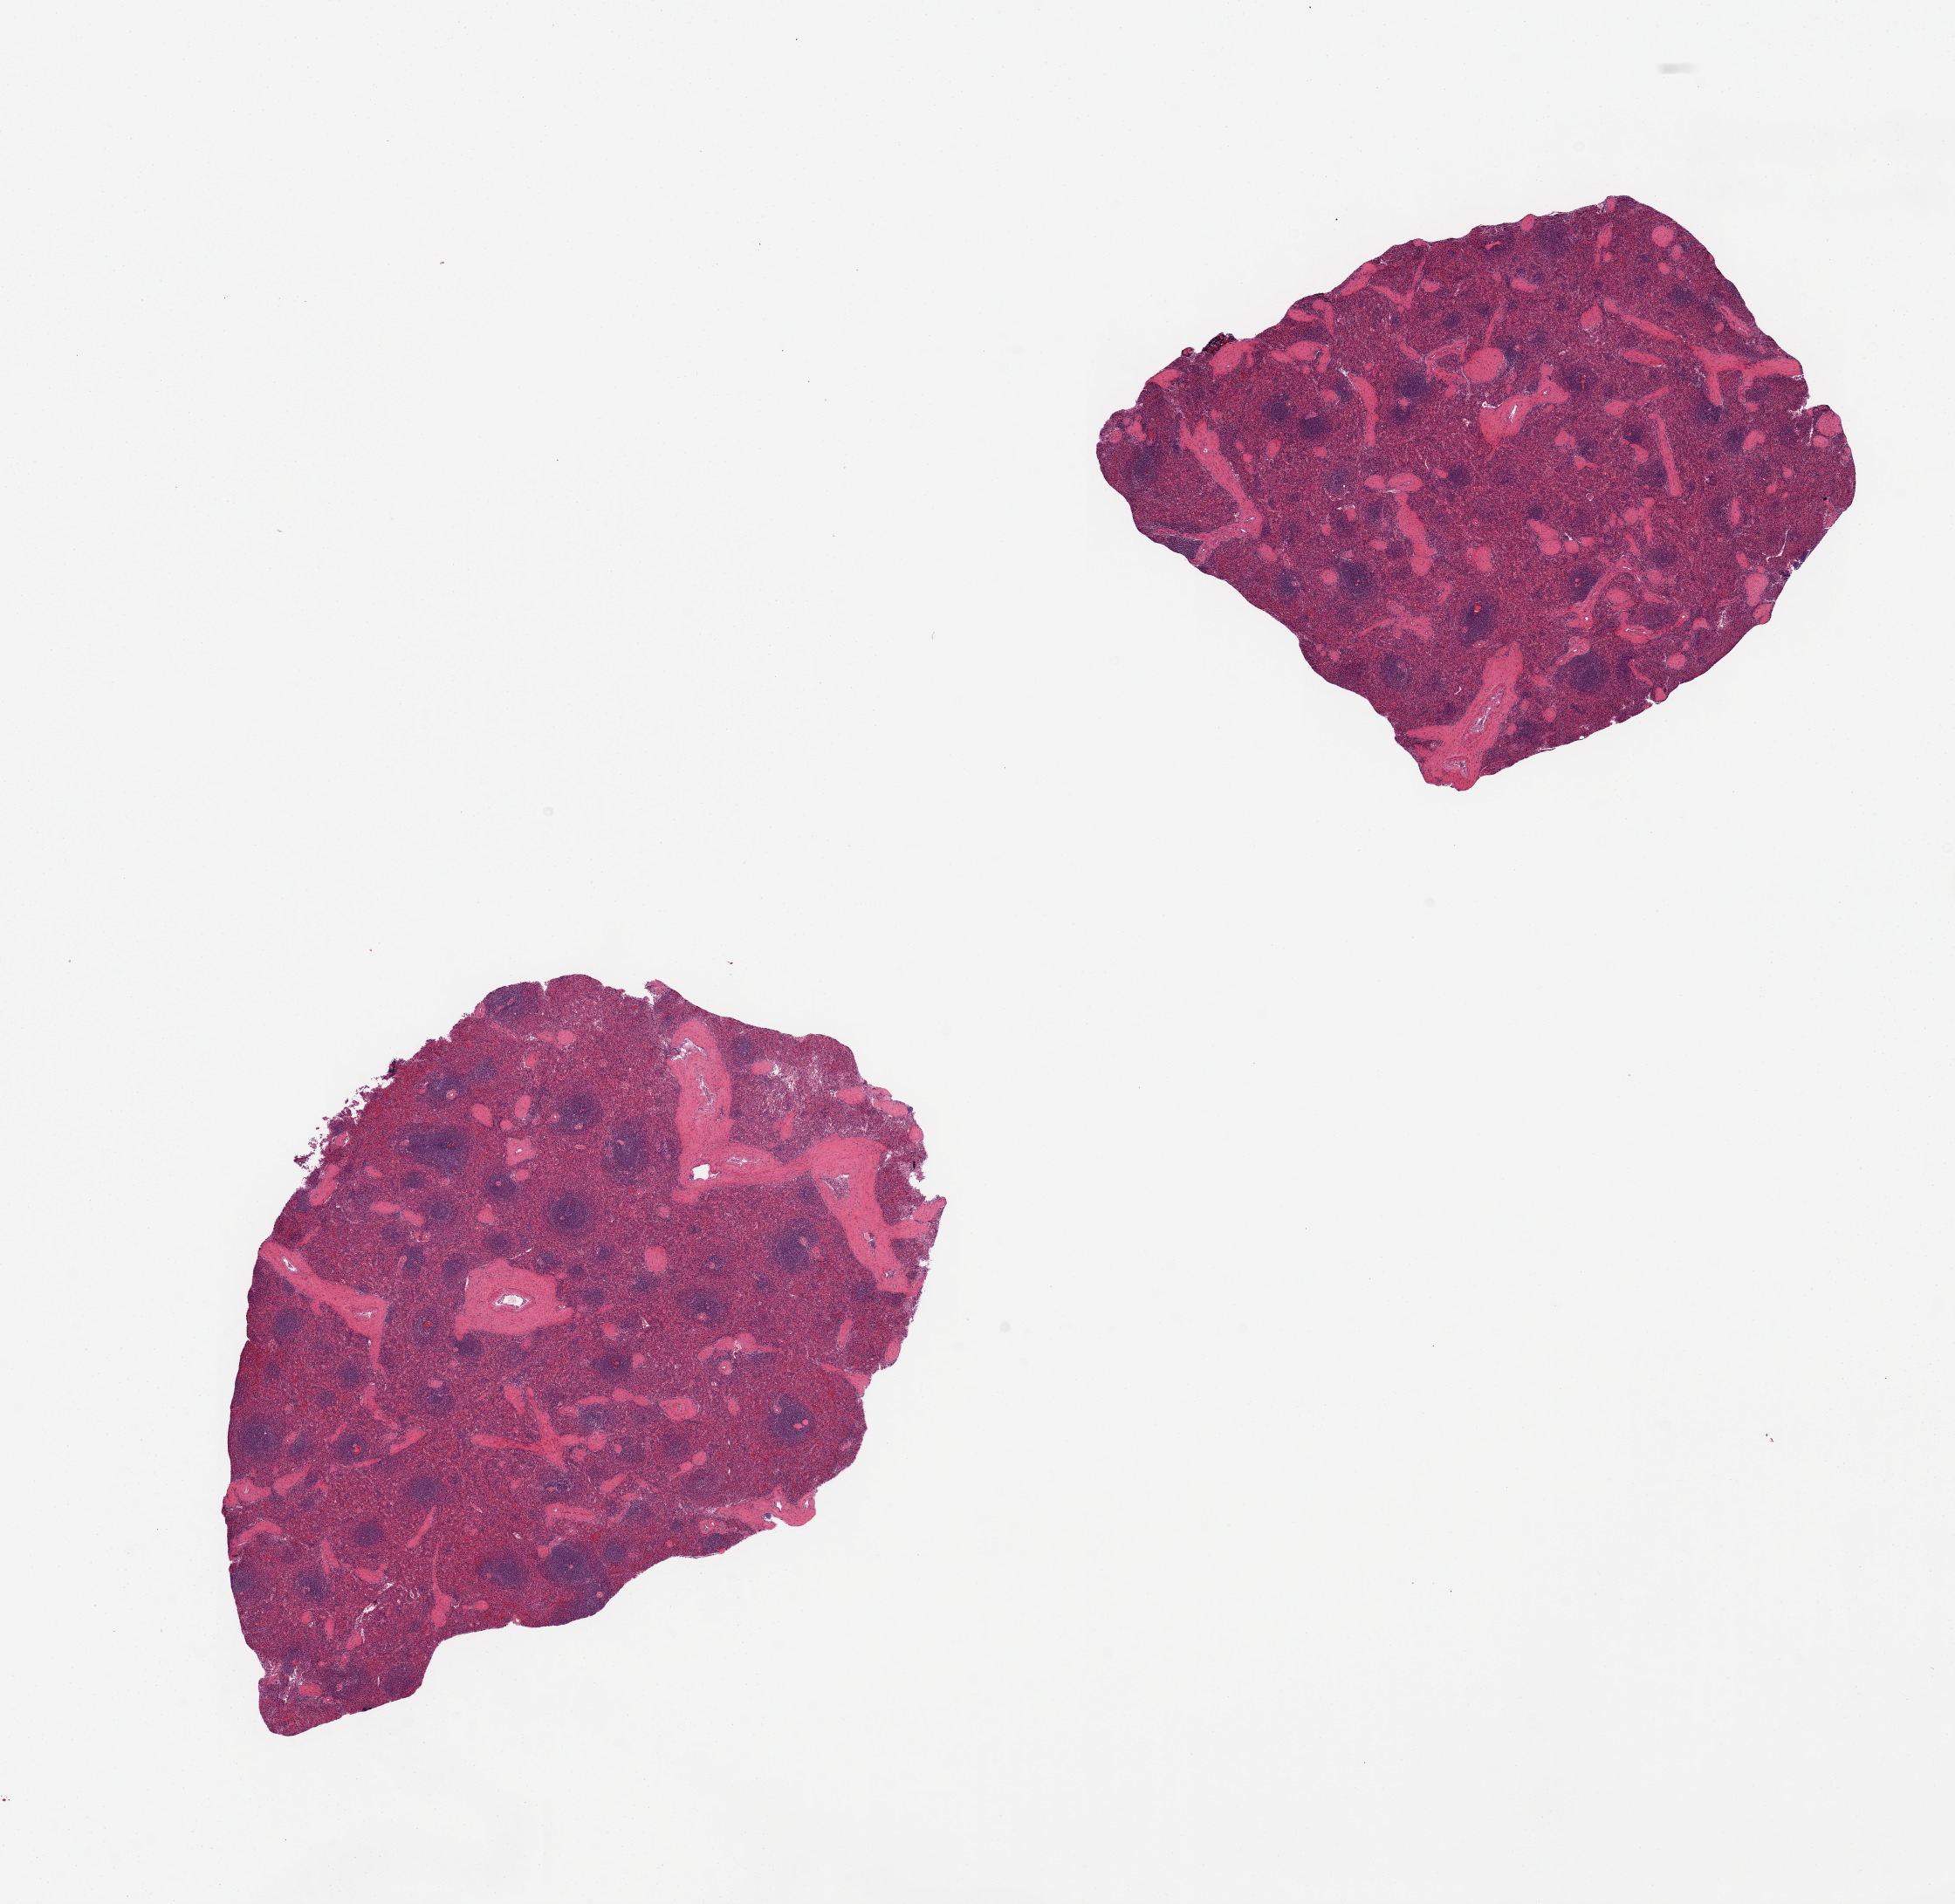
Digitized H&E-stained section — low-resolution overview of the scanned area, about 17.7 x 17.3 mm (from a 20x scan), PAXgene-fixed paraffin-embedded (PFPE) section, section of spleen (target tissue), donor tissue sample. Donor: male.
Review note (as recorded): 2 pieces.